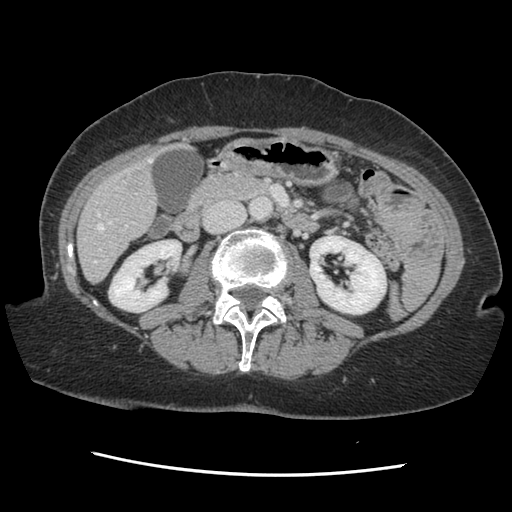
Contrast-enhanced abdominal CT, one axial slice. Slice 52 of 141 in the series (ordered by position). 120 kVp. Soft-tissue window (W 400 / L 40 HU). 512 × 512 image matrix. Female patient, age 61 years. Case-level facts recorded for this patient, not image findings: diagnosis: colorectal cancer liver metastases, imaged before liver resection; multiple liver metastases: no; largest metastasis: 2.4 cm.
Annotated regions visible in this slice (manually delineated by an expert):
- hepatic veins: bounding box (x1, y1, x2, y2) in pixels: (94, 159, 152, 263)
- liver: (78, 152, 162, 282)
- planned liver remnant (the part of the liver to remain after resection): (78, 193, 157, 281)
- portal vein (with intrahepatic branches): (99, 225, 128, 250)
- liver metastasis: (125, 163, 150, 189)